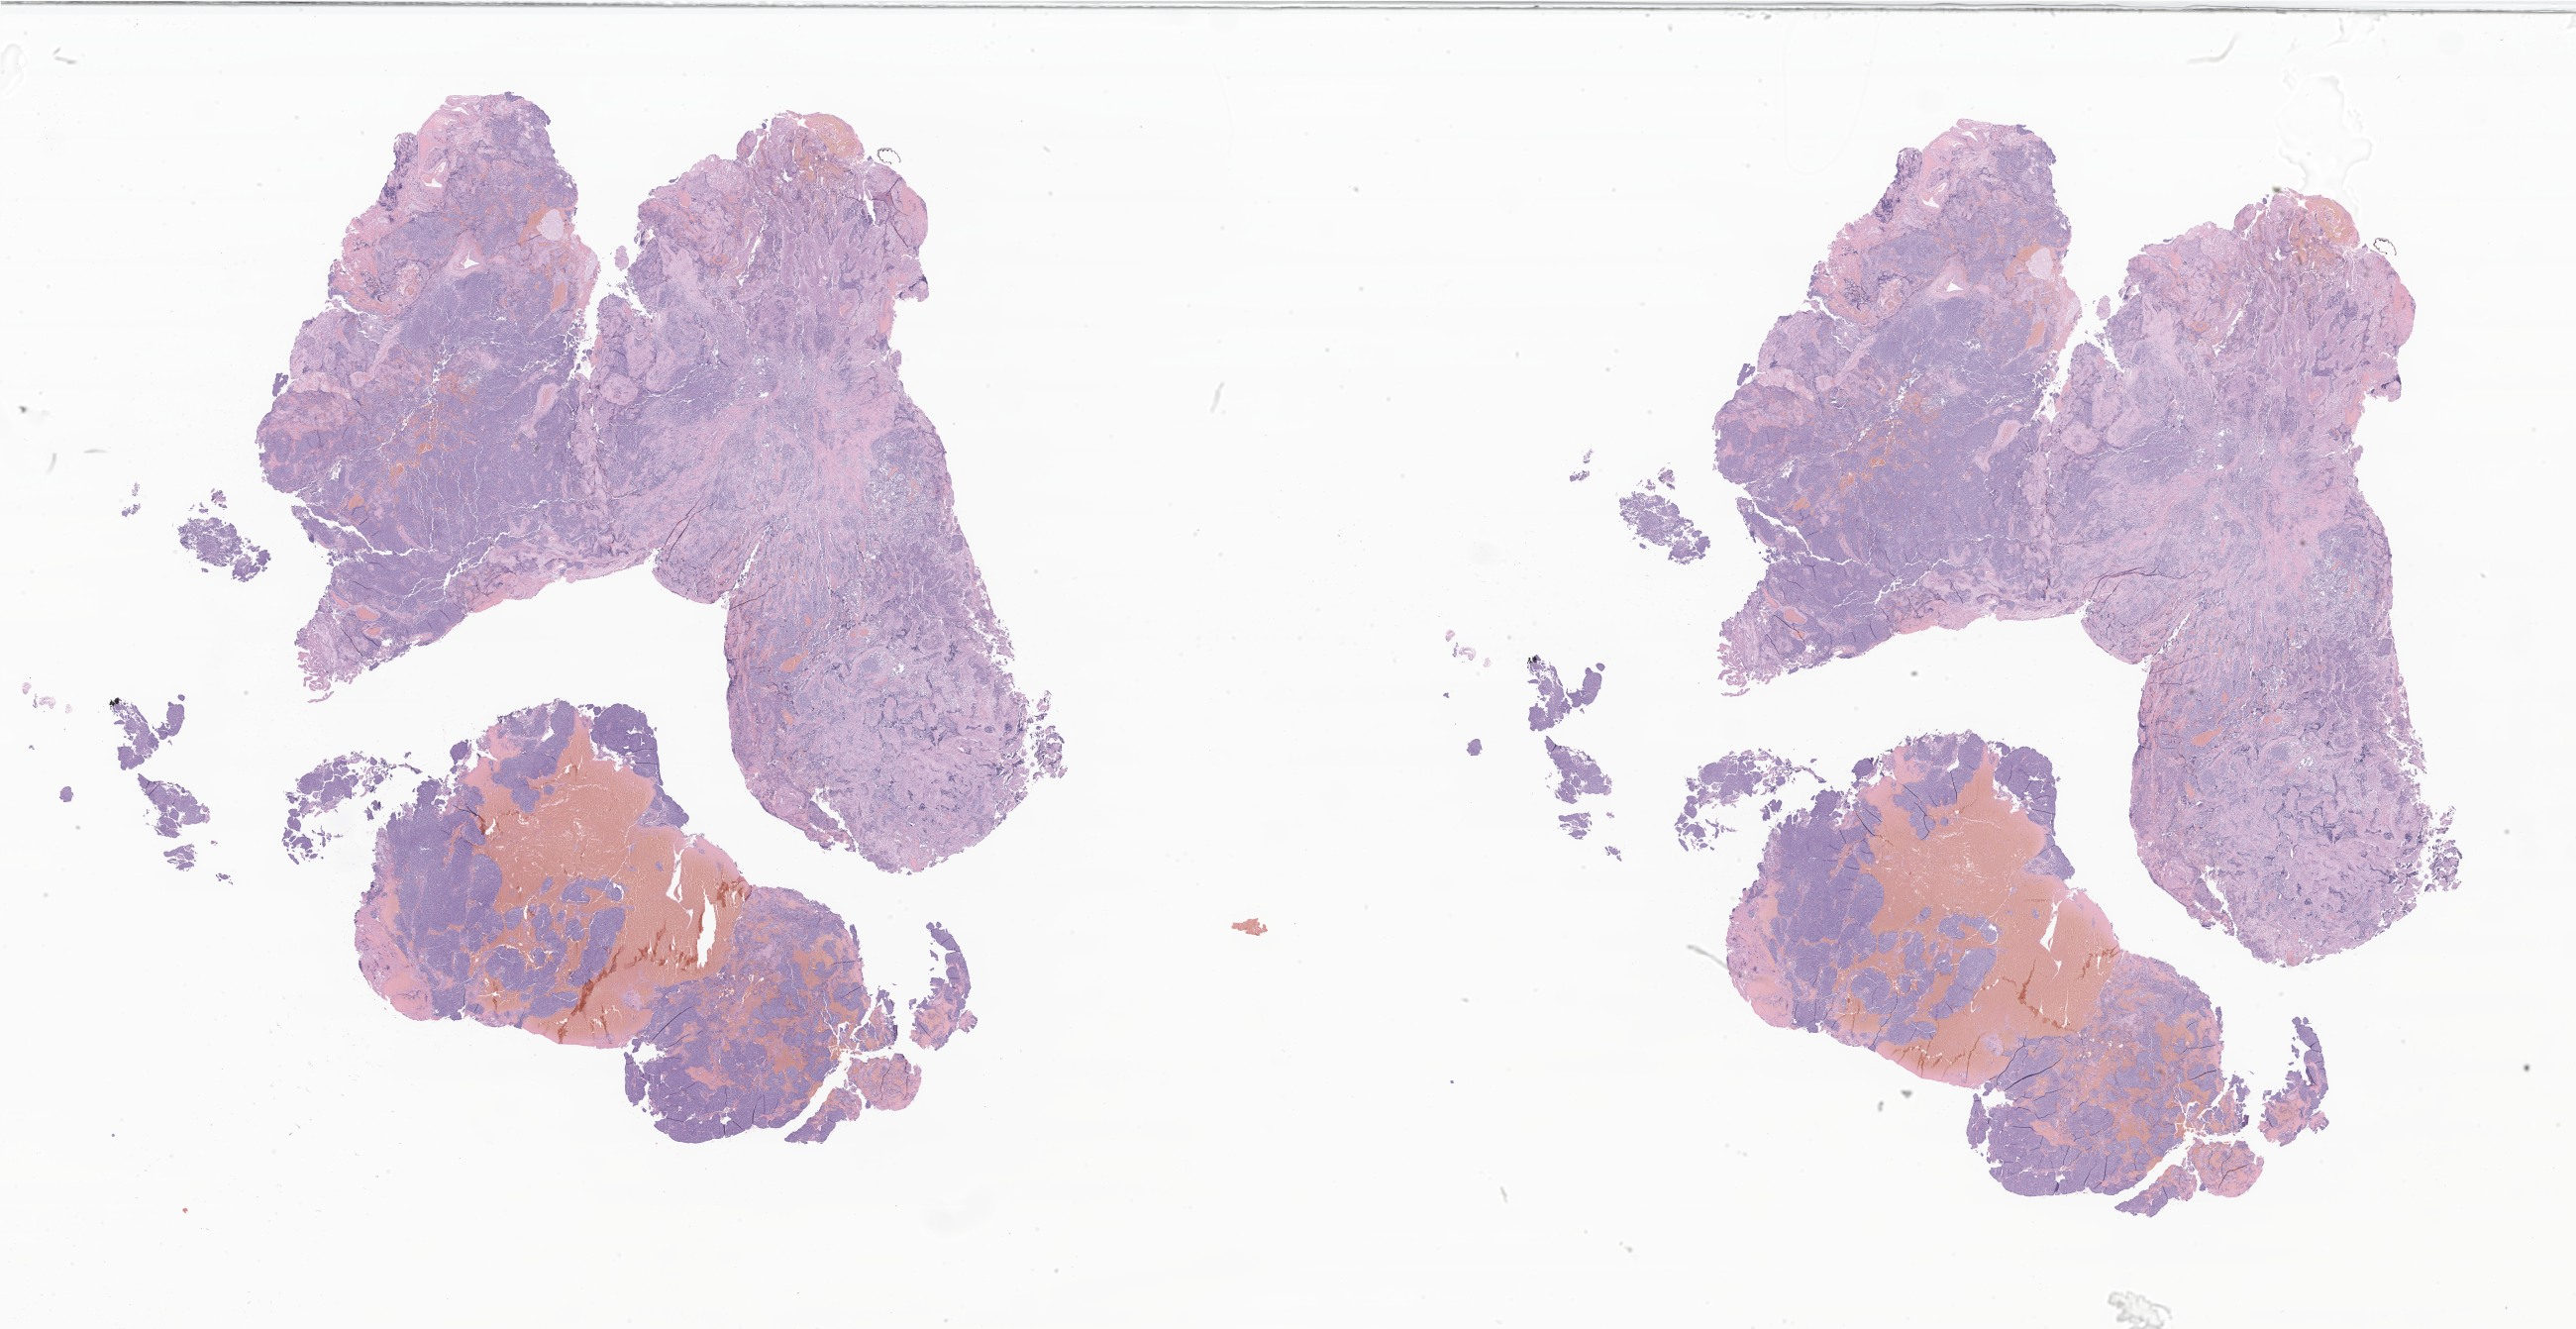
Digitized hematoxylin and eosin (H&E)-stained section of tumor tissue from the brain, low-resolution overview of the scanned area, about 43.9 x 22.6 mm; FFPE section. Patient: male, age 84 months (7 years).
* recorded diagnosis: Medulloblastoma, NOS